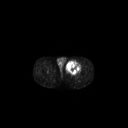
FDG PET of an extremity soft-tissue mass (from a PET/CT study), one axial slice. Slice 255 of 267 in the series (ordered by position). 3.27 mm slice thickness. 128 × 128 image matrix, field of view 700 × 700 mm. Male patient, age 63 years. Case-level facts recorded for this patient, not image findings: histological type: pleiomorphic liposarcoma; grade: high; site of the primary tumour: left thigh.
Annotated regions visible in this slice (expert contour drawn on MRI and transferred to this co-registered scan by the dataset authors):
- gross tumour volume including surrounding oedema: bounding box [x1, y1, x2, y2] px = [66, 60, 81, 73]
- gross tumour volume (mass): [66, 61, 81, 74]